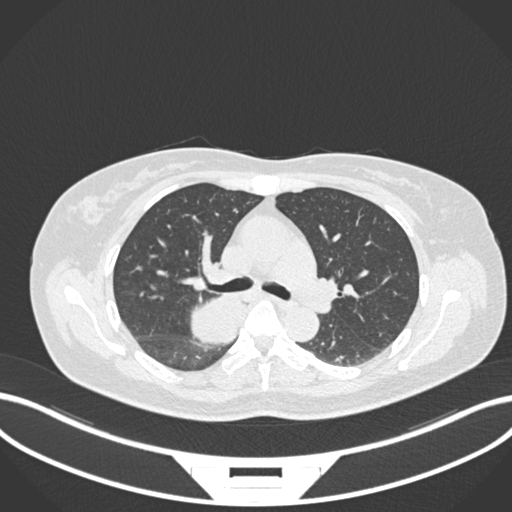
Chest CT, one axial slice. Position 618 of 677 along the scan axis. 120 kVp. Lung window (W 1500 / L -600 HU). 1 mm slice thickness. 512 × 512 image matrix, field of view 400 × 400 mm. Female patient, age 54 years. From the clinical record (not read from this slice): clinical TNM (as recorded): T4 N0 M0.
Outlined on this slice (rectangle marked by the reading radiologist):
- lung tumour (recorded histology: adenocarcinoma): bounding box [x1, y1, x2, y2] px = [183, 282, 250, 347]